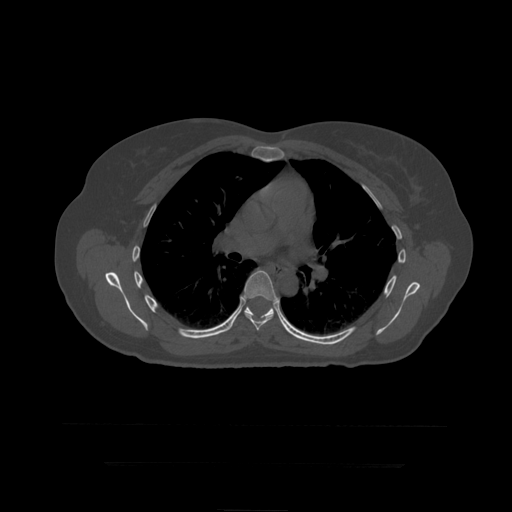
CT including the spine, one axial slice; position 295 of 399 along the scan axis; bone window (W 1800 / L 400 HU); 1.25 mm slice thickness; 512 × 512 image matrix, field of view 450 × 450 mm. Patient age 41 years. From the clinical record (not read from this slice): primary cancer: breast.
Annotated regions visible in this slice (semi-automatically segmented with operator editing):
- T7 vertebra: bounding box <242,271,278,331> (left, top, right, bottom; pixels)
- T8 vertebra: <244,306,274,319>